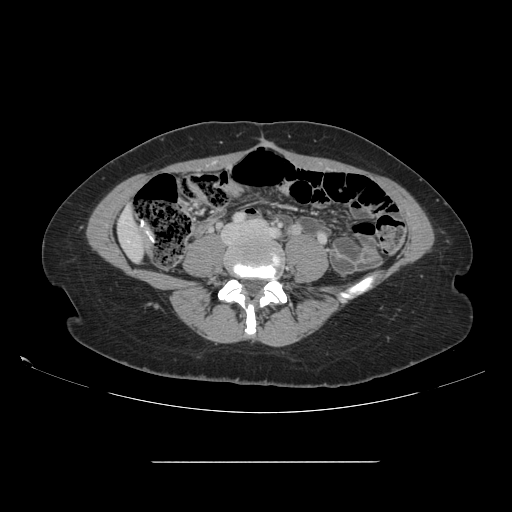
Contrast-enhanced abdominal CT, one axial slice. Slice 12 of 151 in the series (ordered by position). 120 kVp. Intravenous contrast given. Soft-tissue window (W 400 / L 40 HU). 512 × 512 image matrix, field of view 421 × 421 mm. Female patient, age 46 years. From the clinical record (not read from this slice): diagnosis: colorectal cancer liver metastases, imaged before liver resection.
Outlined on this slice (expert manual segmentation):
- liver: bounding box <119,210,145,260> (left, top, right, bottom; pixels)
- planned liver remnant (the part of the liver to remain after resection): <119,211,145,260>